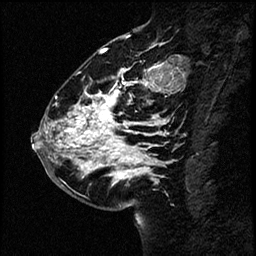
Breast MRI (dynamic contrast-enhanced), one sagittal slice; slice 24 of 60 in the series (ordered by position); dynamic contrast-enhanced study with each time point stored as its own series, time point 2 of 4 at this slice position (early post-contrast, ordered by acquisition time); 1.5 T; TE 4.2 ms, TR 17.6 ms; 2 mm slice thickness; 256 × 256 image matrix, field of view 200 × 200 mm. Patient: female, 43 years. From the clinical record (not read from this slice): setting: breast cancer imaged before/during neoadjuvant chemotherapy.
Outlined on this slice (semi-automatically segmented with operator editing):
- analysis volume of interest (the breast-tissue region the enhancement analysis was run in; not a lesion): box from (x=34, y=59) to (x=169, y=191) px
- tumour enhancement mask (voxels above the 100 % enhancement threshold inside the analysis volume of interest): (x=37, y=65)–(x=164, y=181)